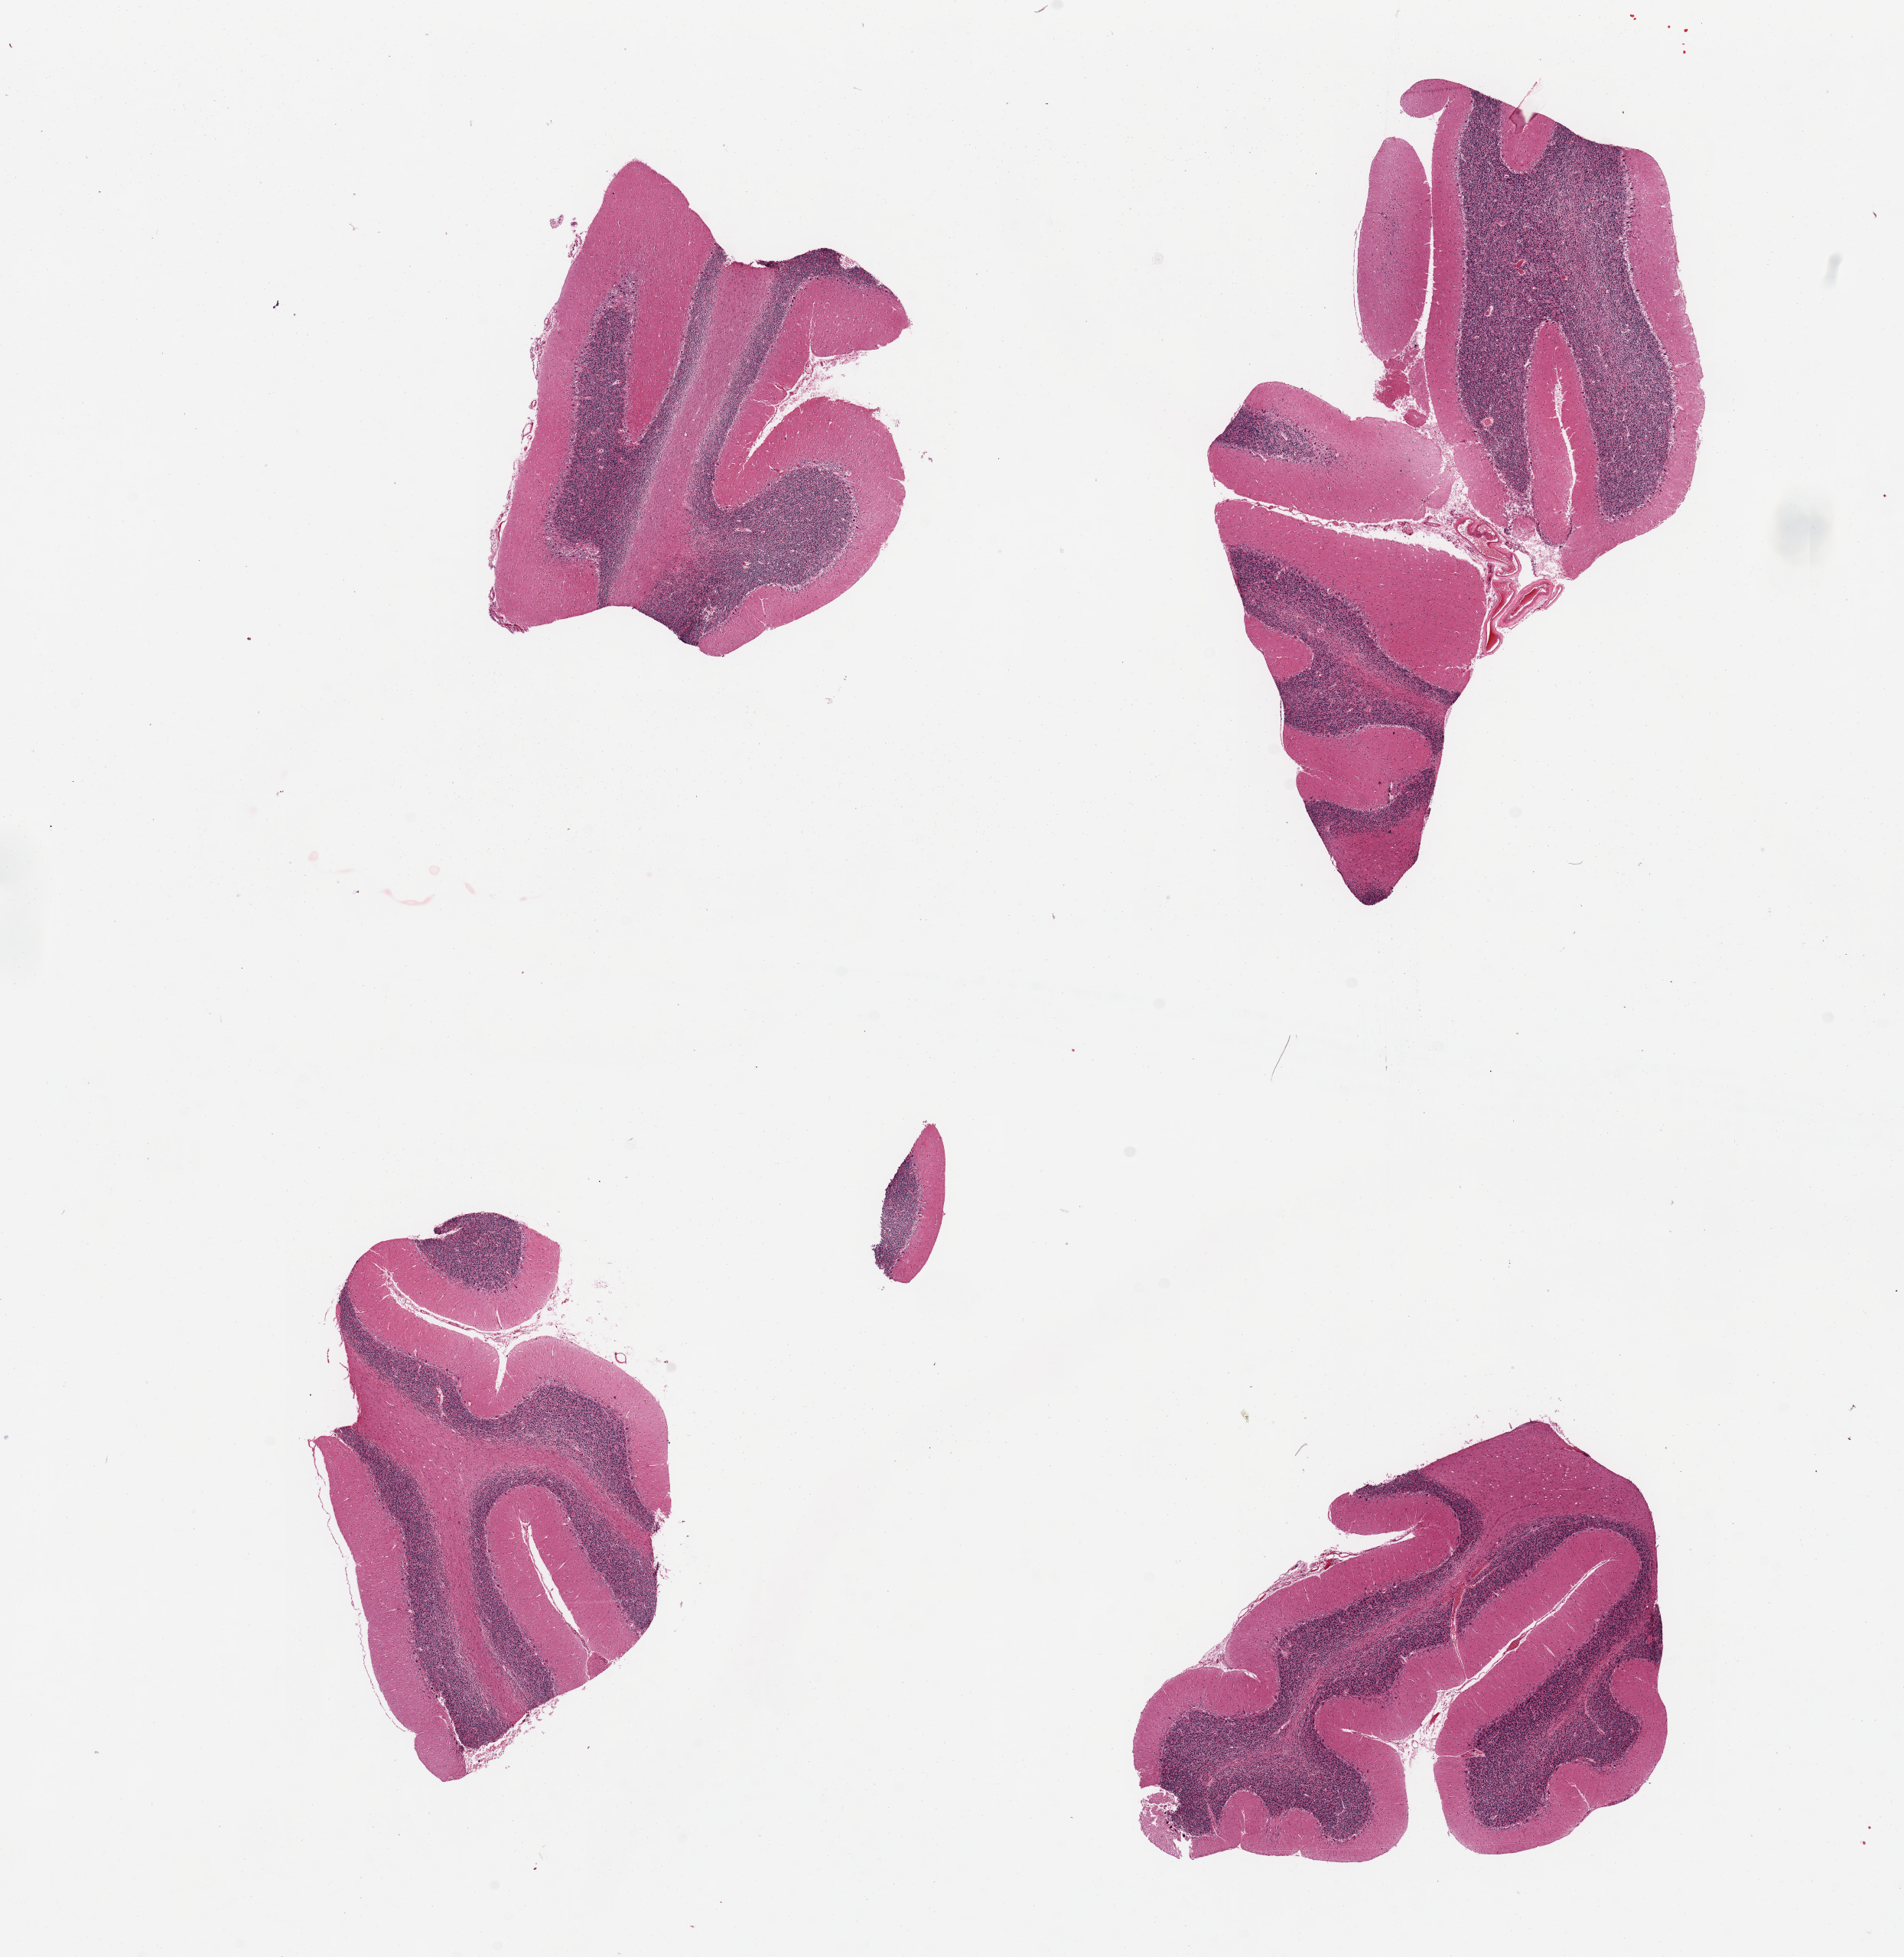
Digitized H&E-stained section — low-resolution overview of the scanned area, about 19.7 x 20.2 mm. PAXgene-fixed paraffin-embedded (PFPE) section. Section of cerebellum (target tissue). Tissue donor sample. Donor: female.
- reviewer comment on this tissue sample: 4 pieces, no abnormalities